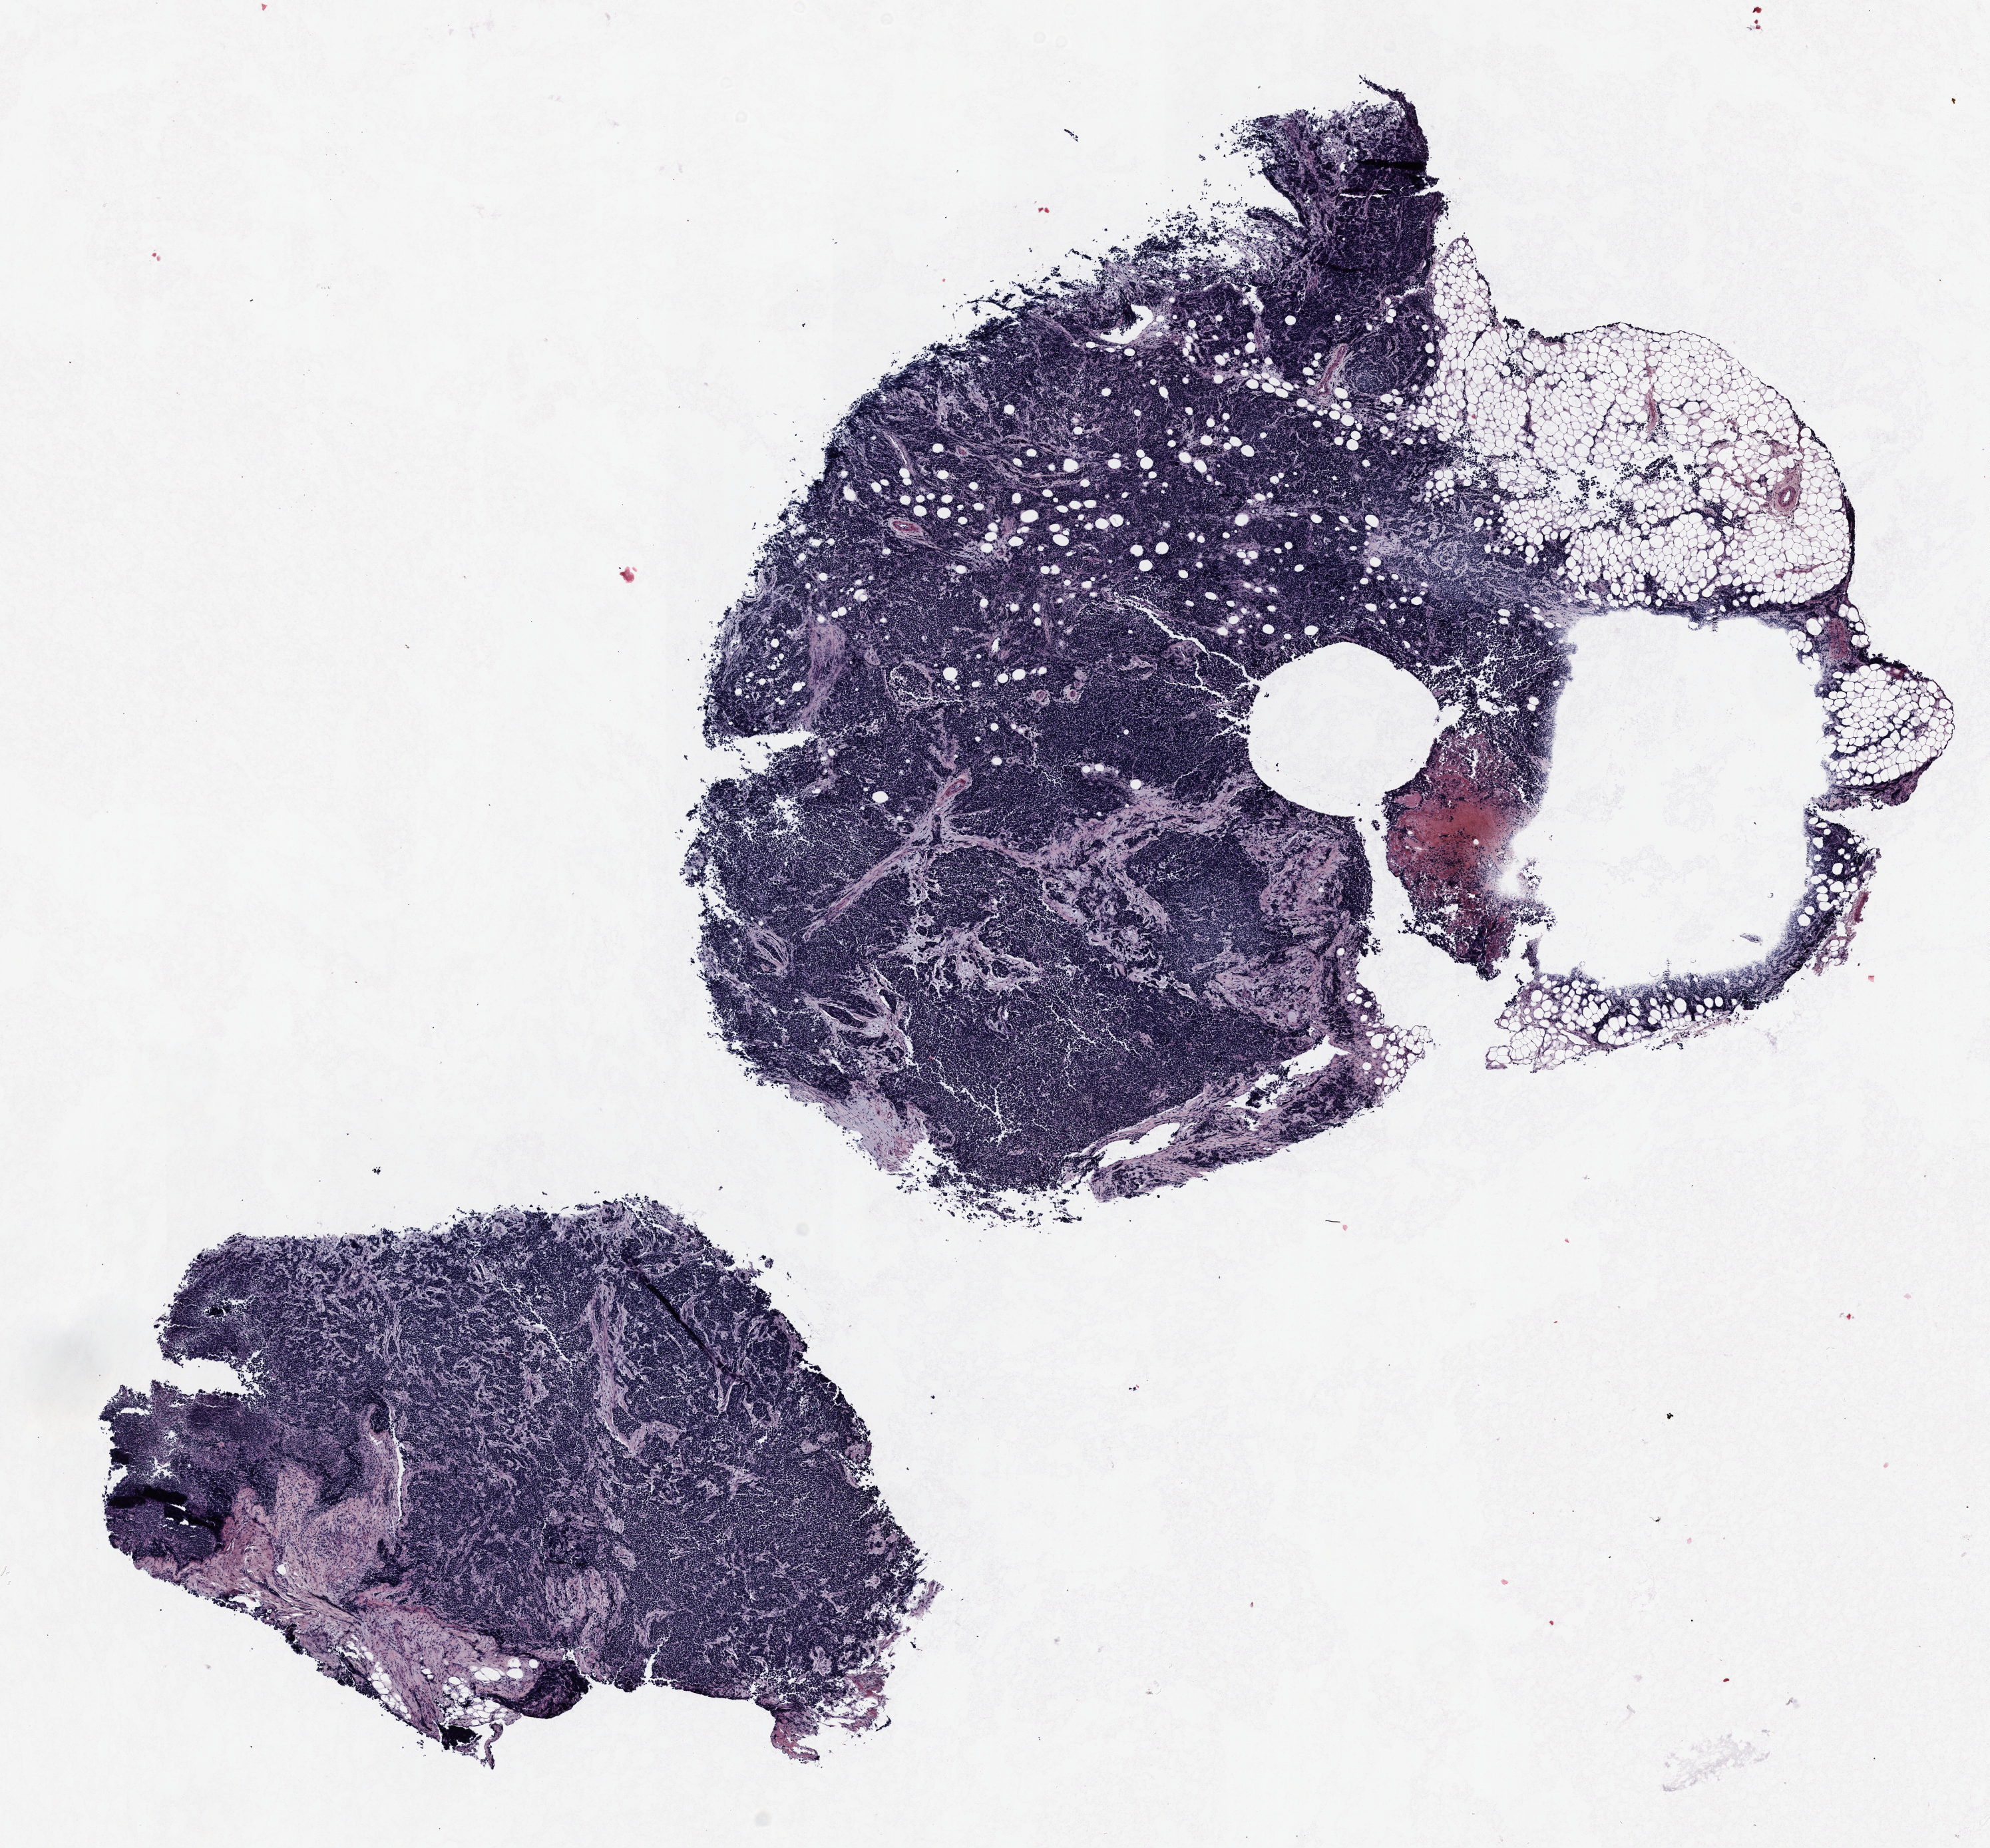
Whole-slide histology image, H&E-stained — shown as a low-resolution overview of the whole scanned area (about 12.0 x 11.2 mm); formalin-fixed paraffin-embedded (FFPE) section; lung tissue. Male, age 64 at enrolment. Former smoker at enrolment. Grade: cannot be assessed (GX).
• stage (AJCC 6th edition): IV
• participant's lung-cancer diagnosis: Small cell carcinoma, NOS
• tumour size (pathology): 100 mm
• primary tumour location (clinical record): left upper lobe
• ICD-O-3 topography: upper lobe of lung (C34.1)